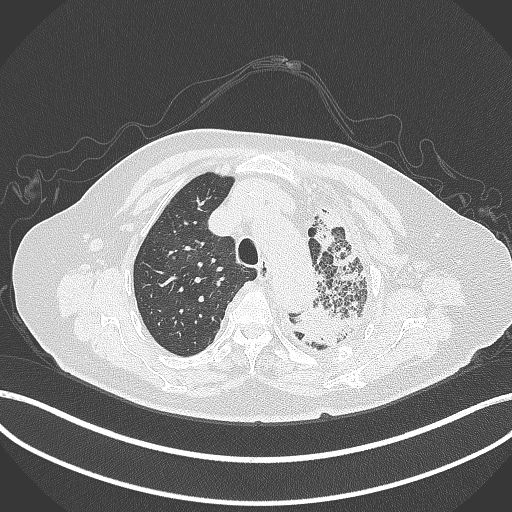
Chest CT, one axial slice; position 305 of 399 along the scan axis; reconstruction kernel B70f; 120 kVp; lung window (W 1500 / L -600 HU); 1 mm slice thickness; 512 × 512 image matrix, field of view 400 × 400 mm. Female patient, age 75 years. Case-level facts recorded for this patient, not image findings: clinical TNM (as recorded): T3 N3 M1.
Structures marked on this image (bounding box drawn by a radiologist):
- lung tumour (recorded histology: adenocarcinoma): box from (x=290, y=298) to (x=361, y=353) px